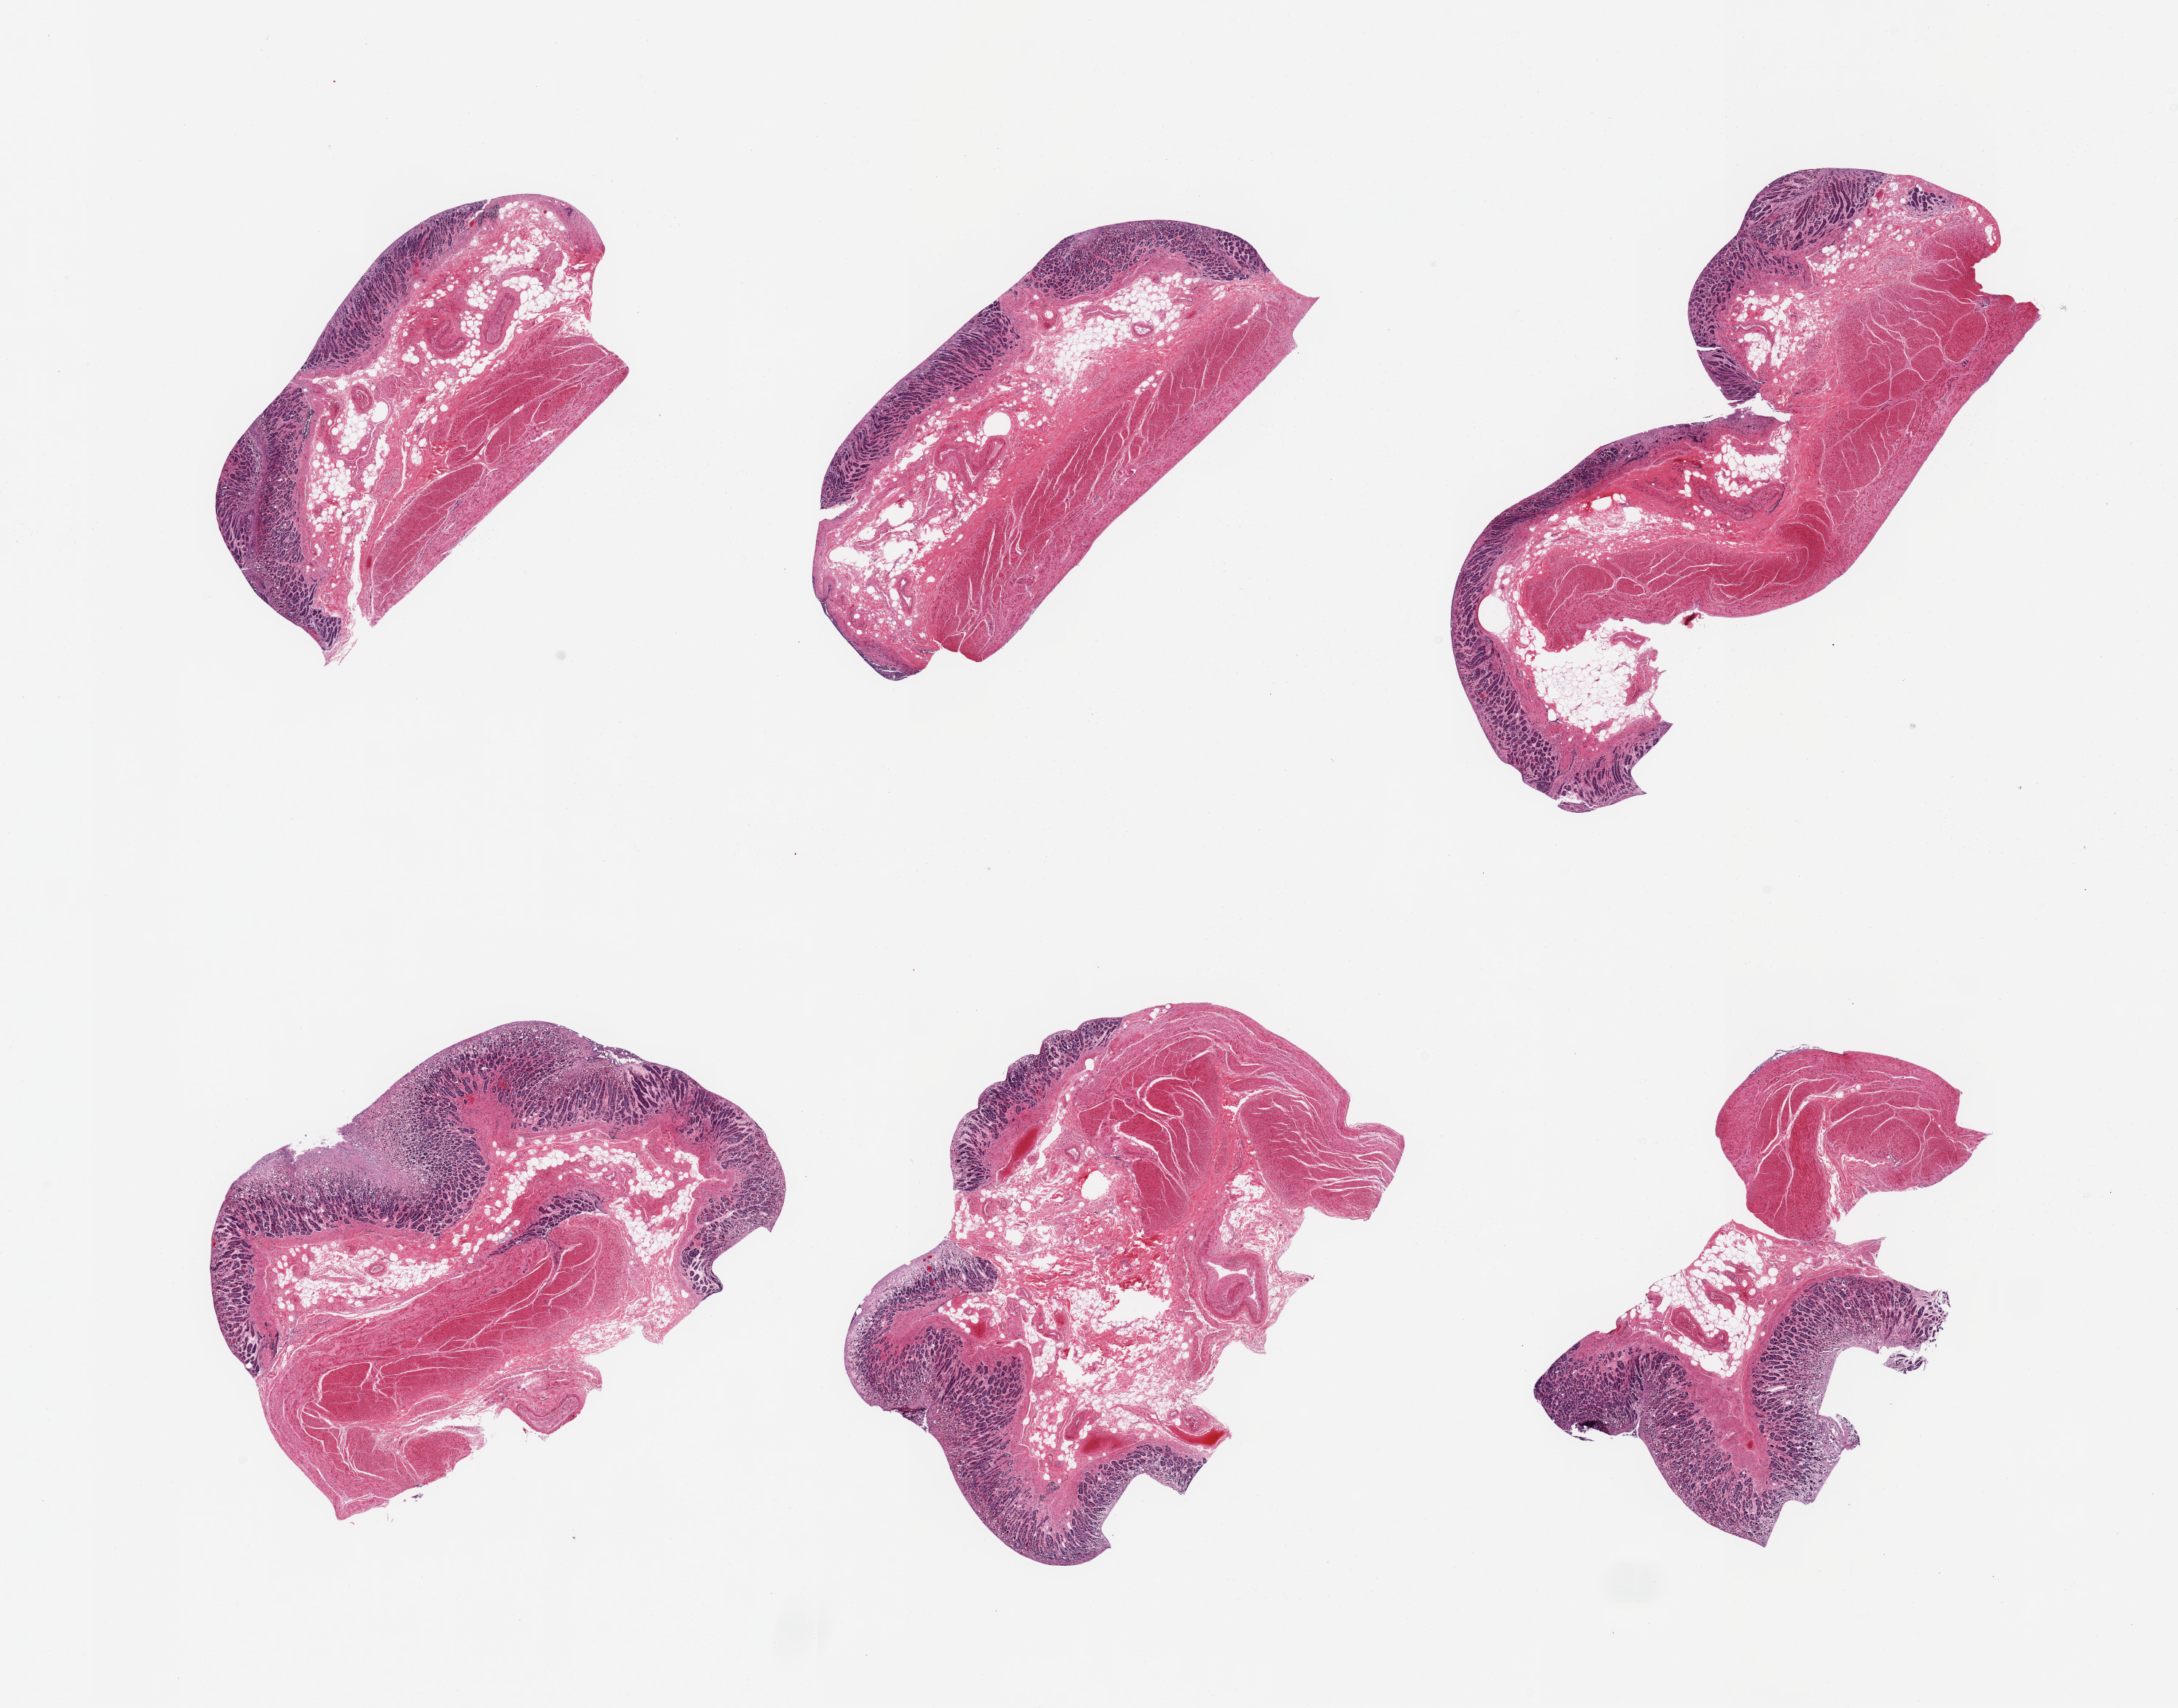
Haematoxylin and eosin whole-slide image — shown as a low-resolution overview of the whole scanned area (about 23.6 x 18.5 mm), PAXgene-fixed, paraffin-embedded tissue, sampled site (target tissue): gastroesophageal junction, donor tissue sample. Male donor.
Reviewer comment on this tissue sample: 6 pieces, ~40% target muscularis, mainly mucosa and fat/serosia.